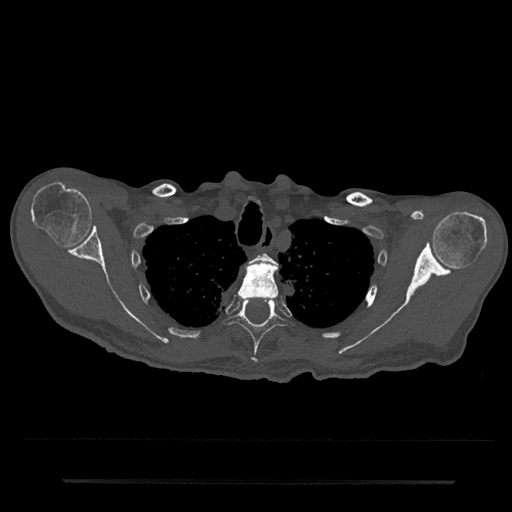
CT including the spine, one axial slice. Position 636 of 797 along the scan axis. 120 kVp. Bone window (W 1800 / L 400 HU). 0.5 mm slice thickness. 512 × 512 image matrix, field of view 427 × 427 mm. Male patient, age 74 years. Case-level facts recorded for this patient, not image findings: primary cancer: prostate.
Outlined on this slice (semi-automatically segmented with operator editing):
- T2 vertebra: bounding box (x1, y1, x2, y2) in pixels: (253, 253, 274, 263)
- T3 vertebra: (238, 261, 279, 298)
- T4 vertebra: (226, 298, 286, 363)